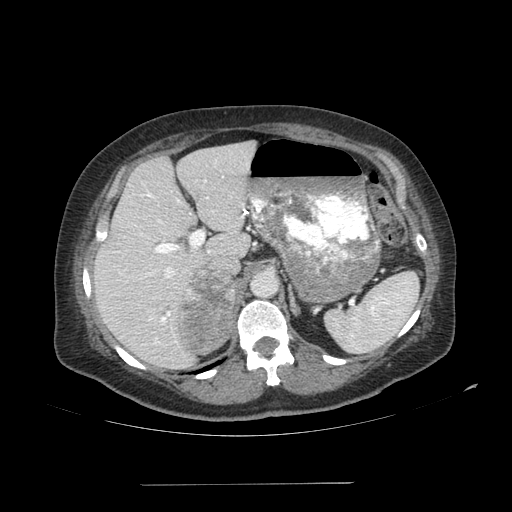
Contrast-enhanced abdominal CT, one axial slice; slice 70 of 113 in the series (ordered by position); soft-tissue window (W 400 / L 40 HU); 2.5 mm slice thickness; 512 × 512 image matrix, field of view 440 × 440 mm. Female patient, age 67 years. From the clinical record (not read from this slice): diagnosis: adrenocortical carcinoma; tumour side: right adrenal.
Outlined on this slice (semi-automatic segmentation, software-assisted and operator-edited):
- mass: box from (x=180, y=272) to (x=237, y=353) px